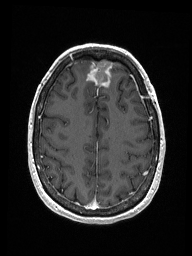
Brain MRI from a brain-tumour surgery series, one axial slice. T1-weighted post-contrast. 1 mm slice thickness. 192 × 256 image matrix. From the clinical record (not read from this slice): histopathology: Metastastic Carcinoma from Breast primary; tumour location: Right Frontal.
Outlined on this slice (outlined manually by an expert reader):
- previous resection cavity: bounding box (x1, y1, x2, y2) in pixels: (90, 60, 113, 85)